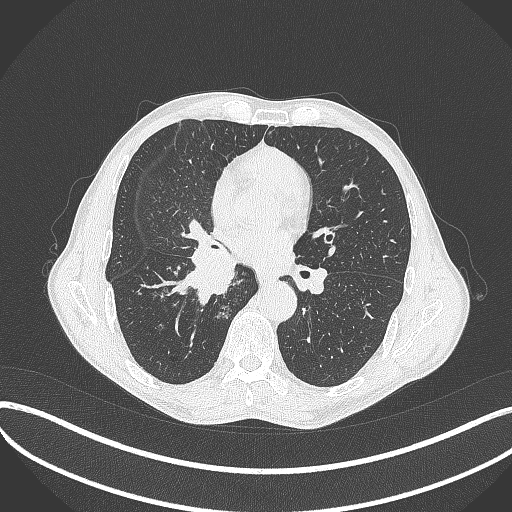
Chest CT, one axial slice; position 218 of 481 along the scan axis; reconstruction kernel B70f; 120 kVp; lung window (W 1500 / L -600 HU); 512 × 512 image matrix. Male patient, age 65 years. Case-level facts recorded for this patient, not image findings: clinical TNM (as recorded): T2a N0 M0; histopathological grade: G2.
Outlined on this slice (bounding box drawn by a radiologist):
- lung tumour (recorded histology: squamous cell carcinoma): bounding box [x1, y1, x2, y2] px = [179, 244, 245, 304]